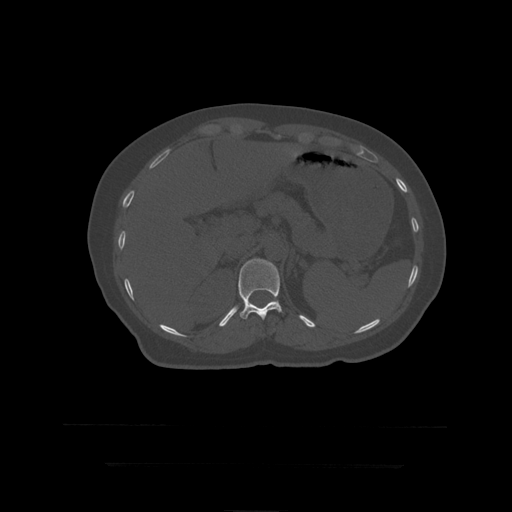
CT including the spine, one axial slice. Slice 198 of 399 in the series (ordered by position). Bone window (W 1800 / L 400 HU). 1.25 mm slice thickness. 512 × 512 image matrix, field of view 450 × 450 mm. Patient age 41 years. From the clinical record (not read from this slice): primary cancer: breast.
Annotated regions visible in this slice (semi-automatic segmentation, software-assisted and operator-edited):
- T12 vertebra: bounding box <238,259,283,320> (left, top, right, bottom; pixels)